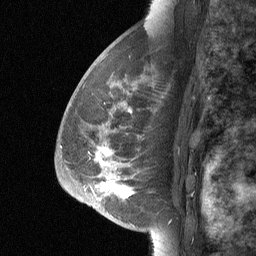
Breast MRI (dynamic contrast-enhanced), one sagittal slice. Position 42 of 64 along the scan axis. Dynamic contrast-enhanced study with each time point stored as its own series, time point 2 of 3 at this slice position (early post-contrast, ordered by acquisition time). 1.5 T. TE 4.8 ms, TR 27 ms. 256 × 256 image matrix. Female patient, age 56 years. From the clinical record (not read from this slice): setting: breast cancer imaged before/during neoadjuvant chemotherapy; receptor status: HER2-positive.
Structures marked on this image (semi-automatically segmented with operator editing):
- analysis volume of interest (the breast-tissue region the enhancement analysis was run in; not a lesion): bounding box <68,83,168,214> (left, top, right, bottom; pixels)
- tumour enhancement mask (voxels above the 90 % enhancement threshold inside the analysis volume of interest): <102,148,131,196>